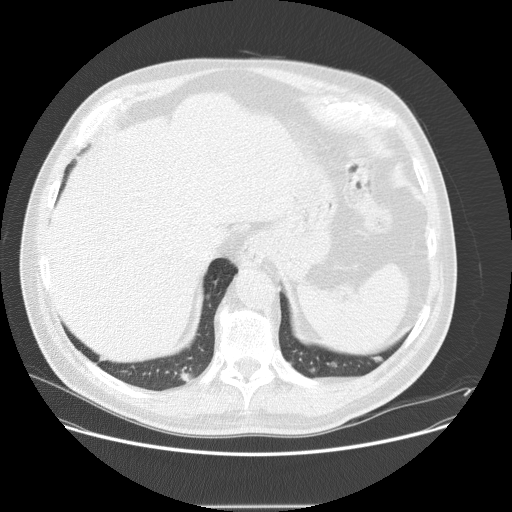
Chest CT (low-dose screening protocol), one axial image. Baseline screening round. Lung window (W 1500 / L -600 HU). Standard (soft-tissue) reconstruction kernel (STANDARD). Slice 110 of 143 in the series. Male participant, aged 61 years at enrolment. Current smoker at enrolment.
Expert reader's lesion annotation, bounding box (x1, y1, x2, y2) in pixels: (163, 362, 202, 399). The screening reader recorded 2 non-calcified nodules or masses ≥4 mm on this exam (left lower lobe, right lower lobe); which of them this box marks is not recorded. Official screen result: positive, change unspecified: nodule(s) >= 4 mm or enlarging nodule(s), mass(es), or other non-specific abnormalities suspicious for lung cancer. Participant outcome: lung cancer diagnosed 41 days after this screen — bronchiolo-alveolar carcinoma, mucinous, right lower lobe, well differentiated (G1), stage IV (AJCC 6th edition), 23 mm at pathology.